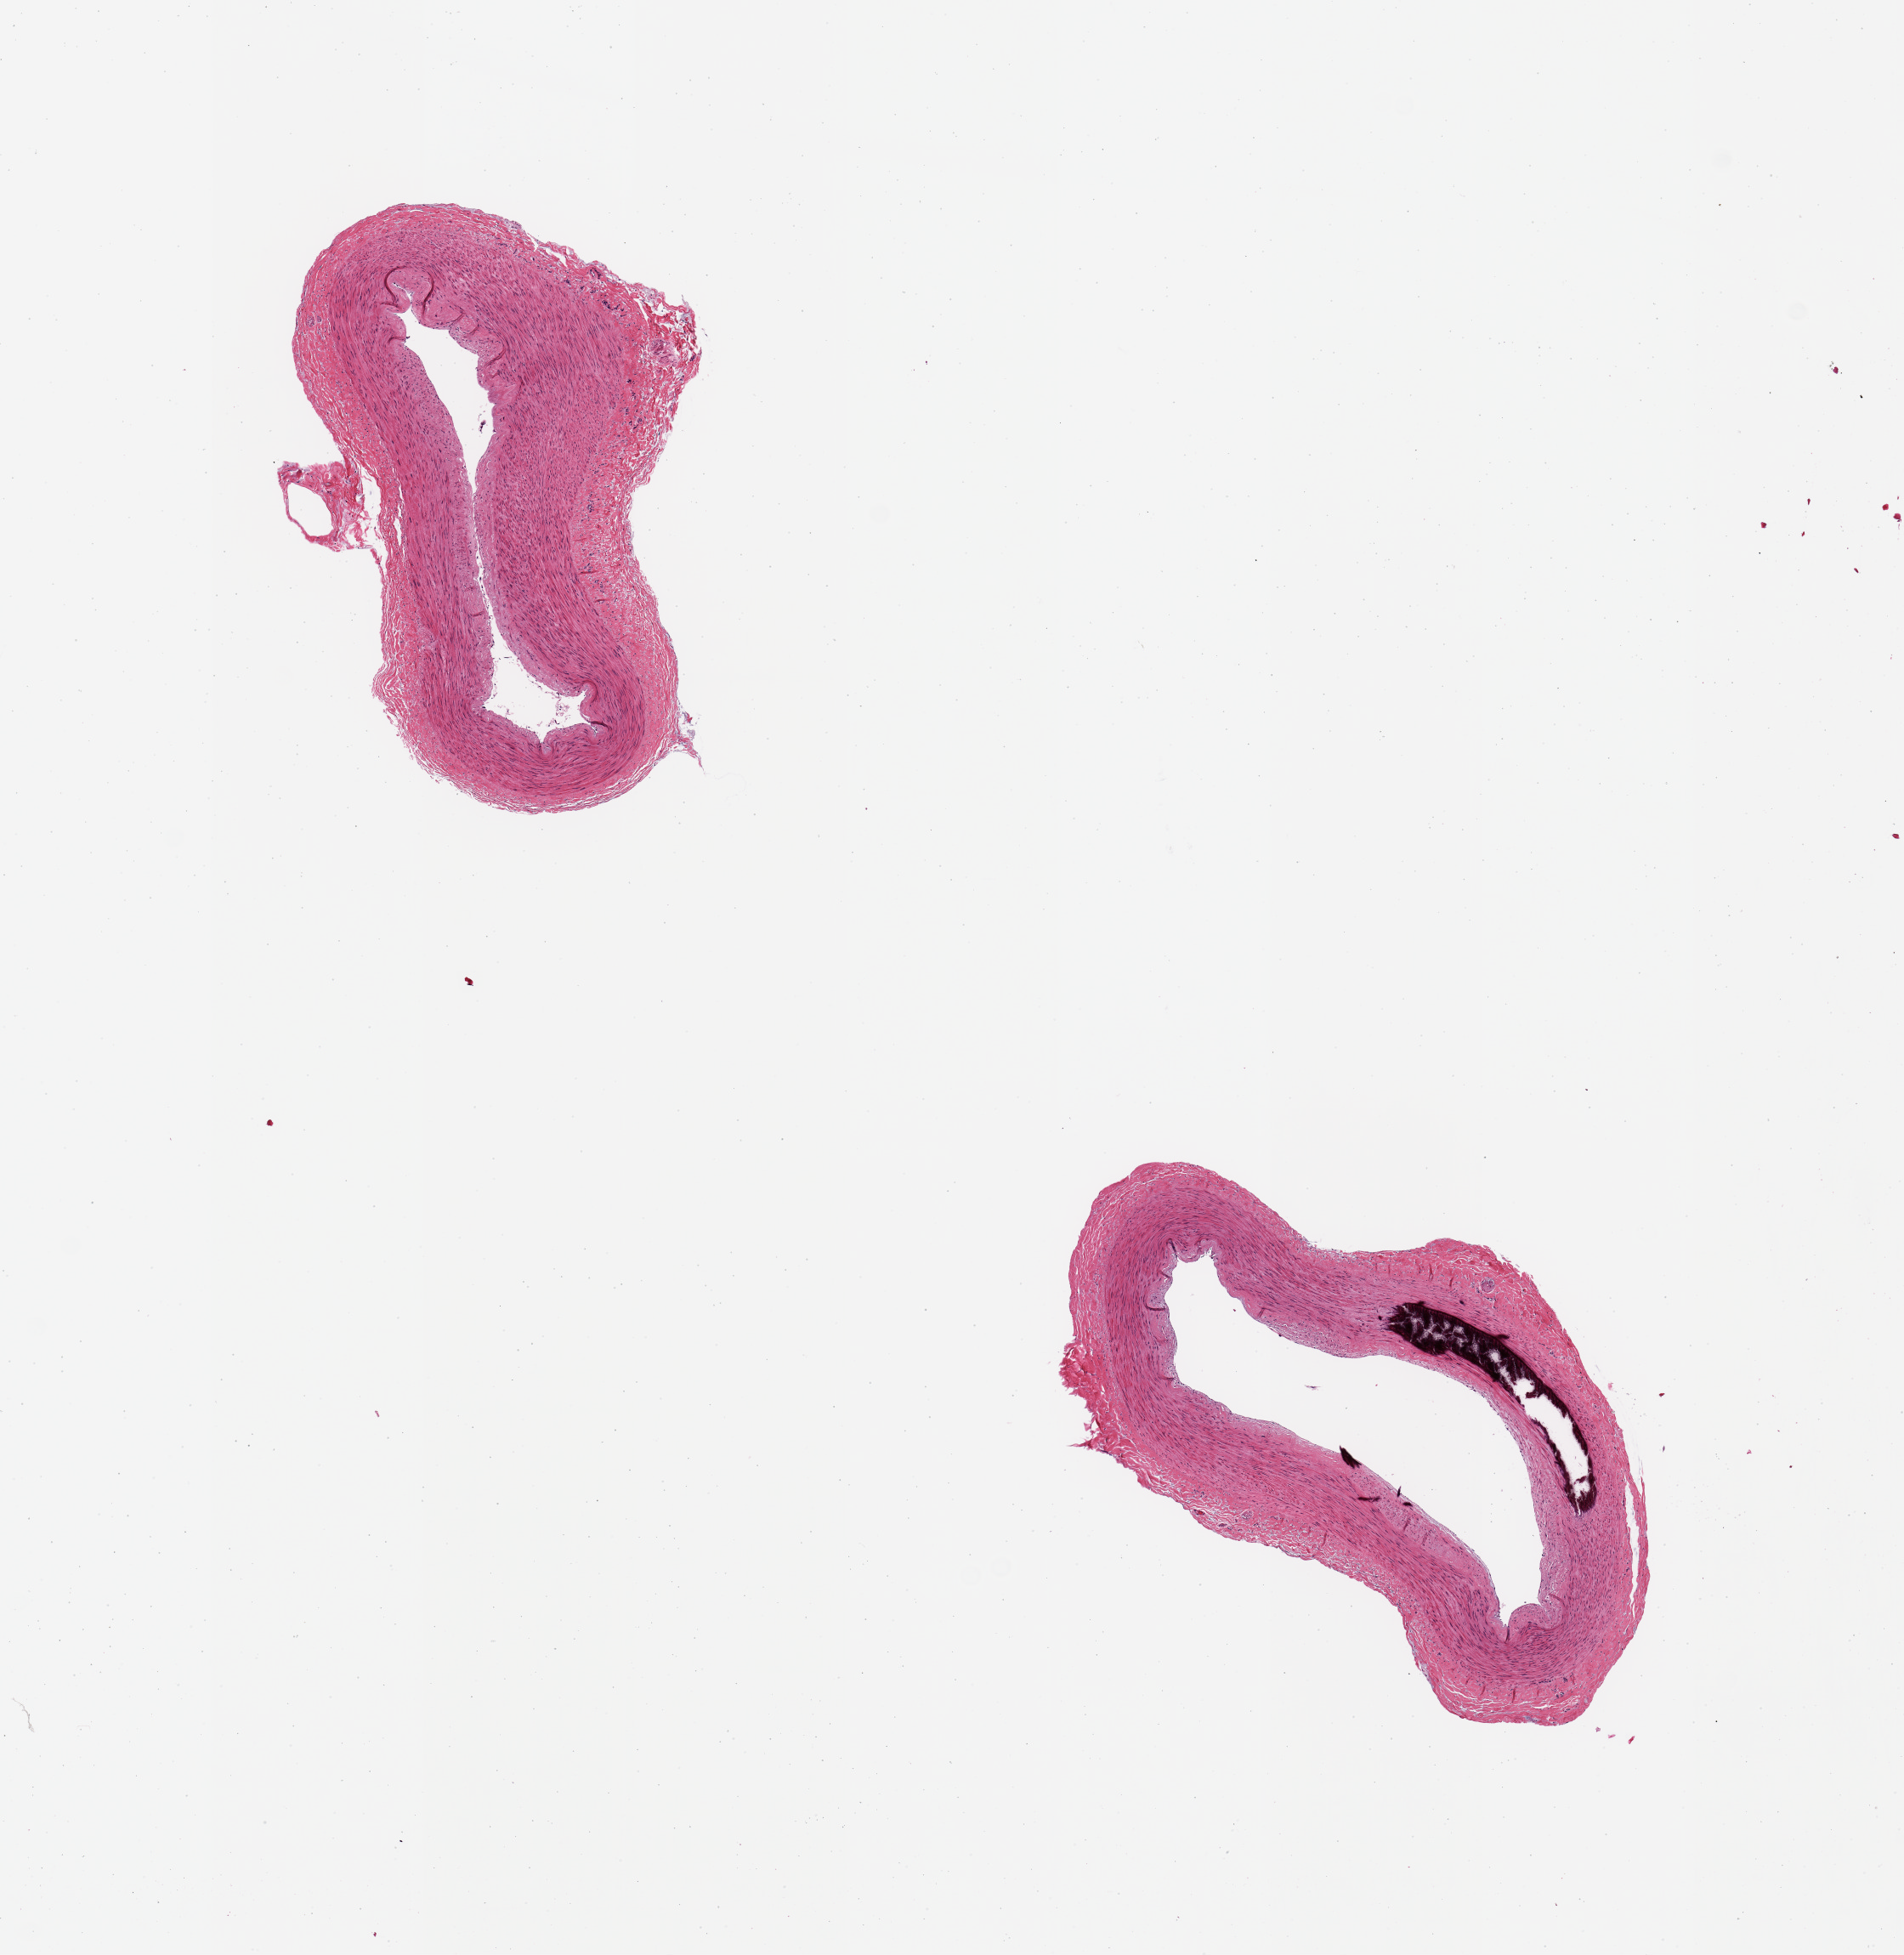
Digitized haematoxylin and eosin-stained section, whole scanned area (about 8.9 x 9.1 mm, from a 20x scan) shown as a low-resolution overview; PAXgene-fixed, paraffin-embedded tissue; section of tibial artery (target tissue); tissue donor sample. Donor: male.
• reviewer comment on this tissue sample: 2 pieces, no significant atherosis or adherent fat; focal Monckeberg sclerosis